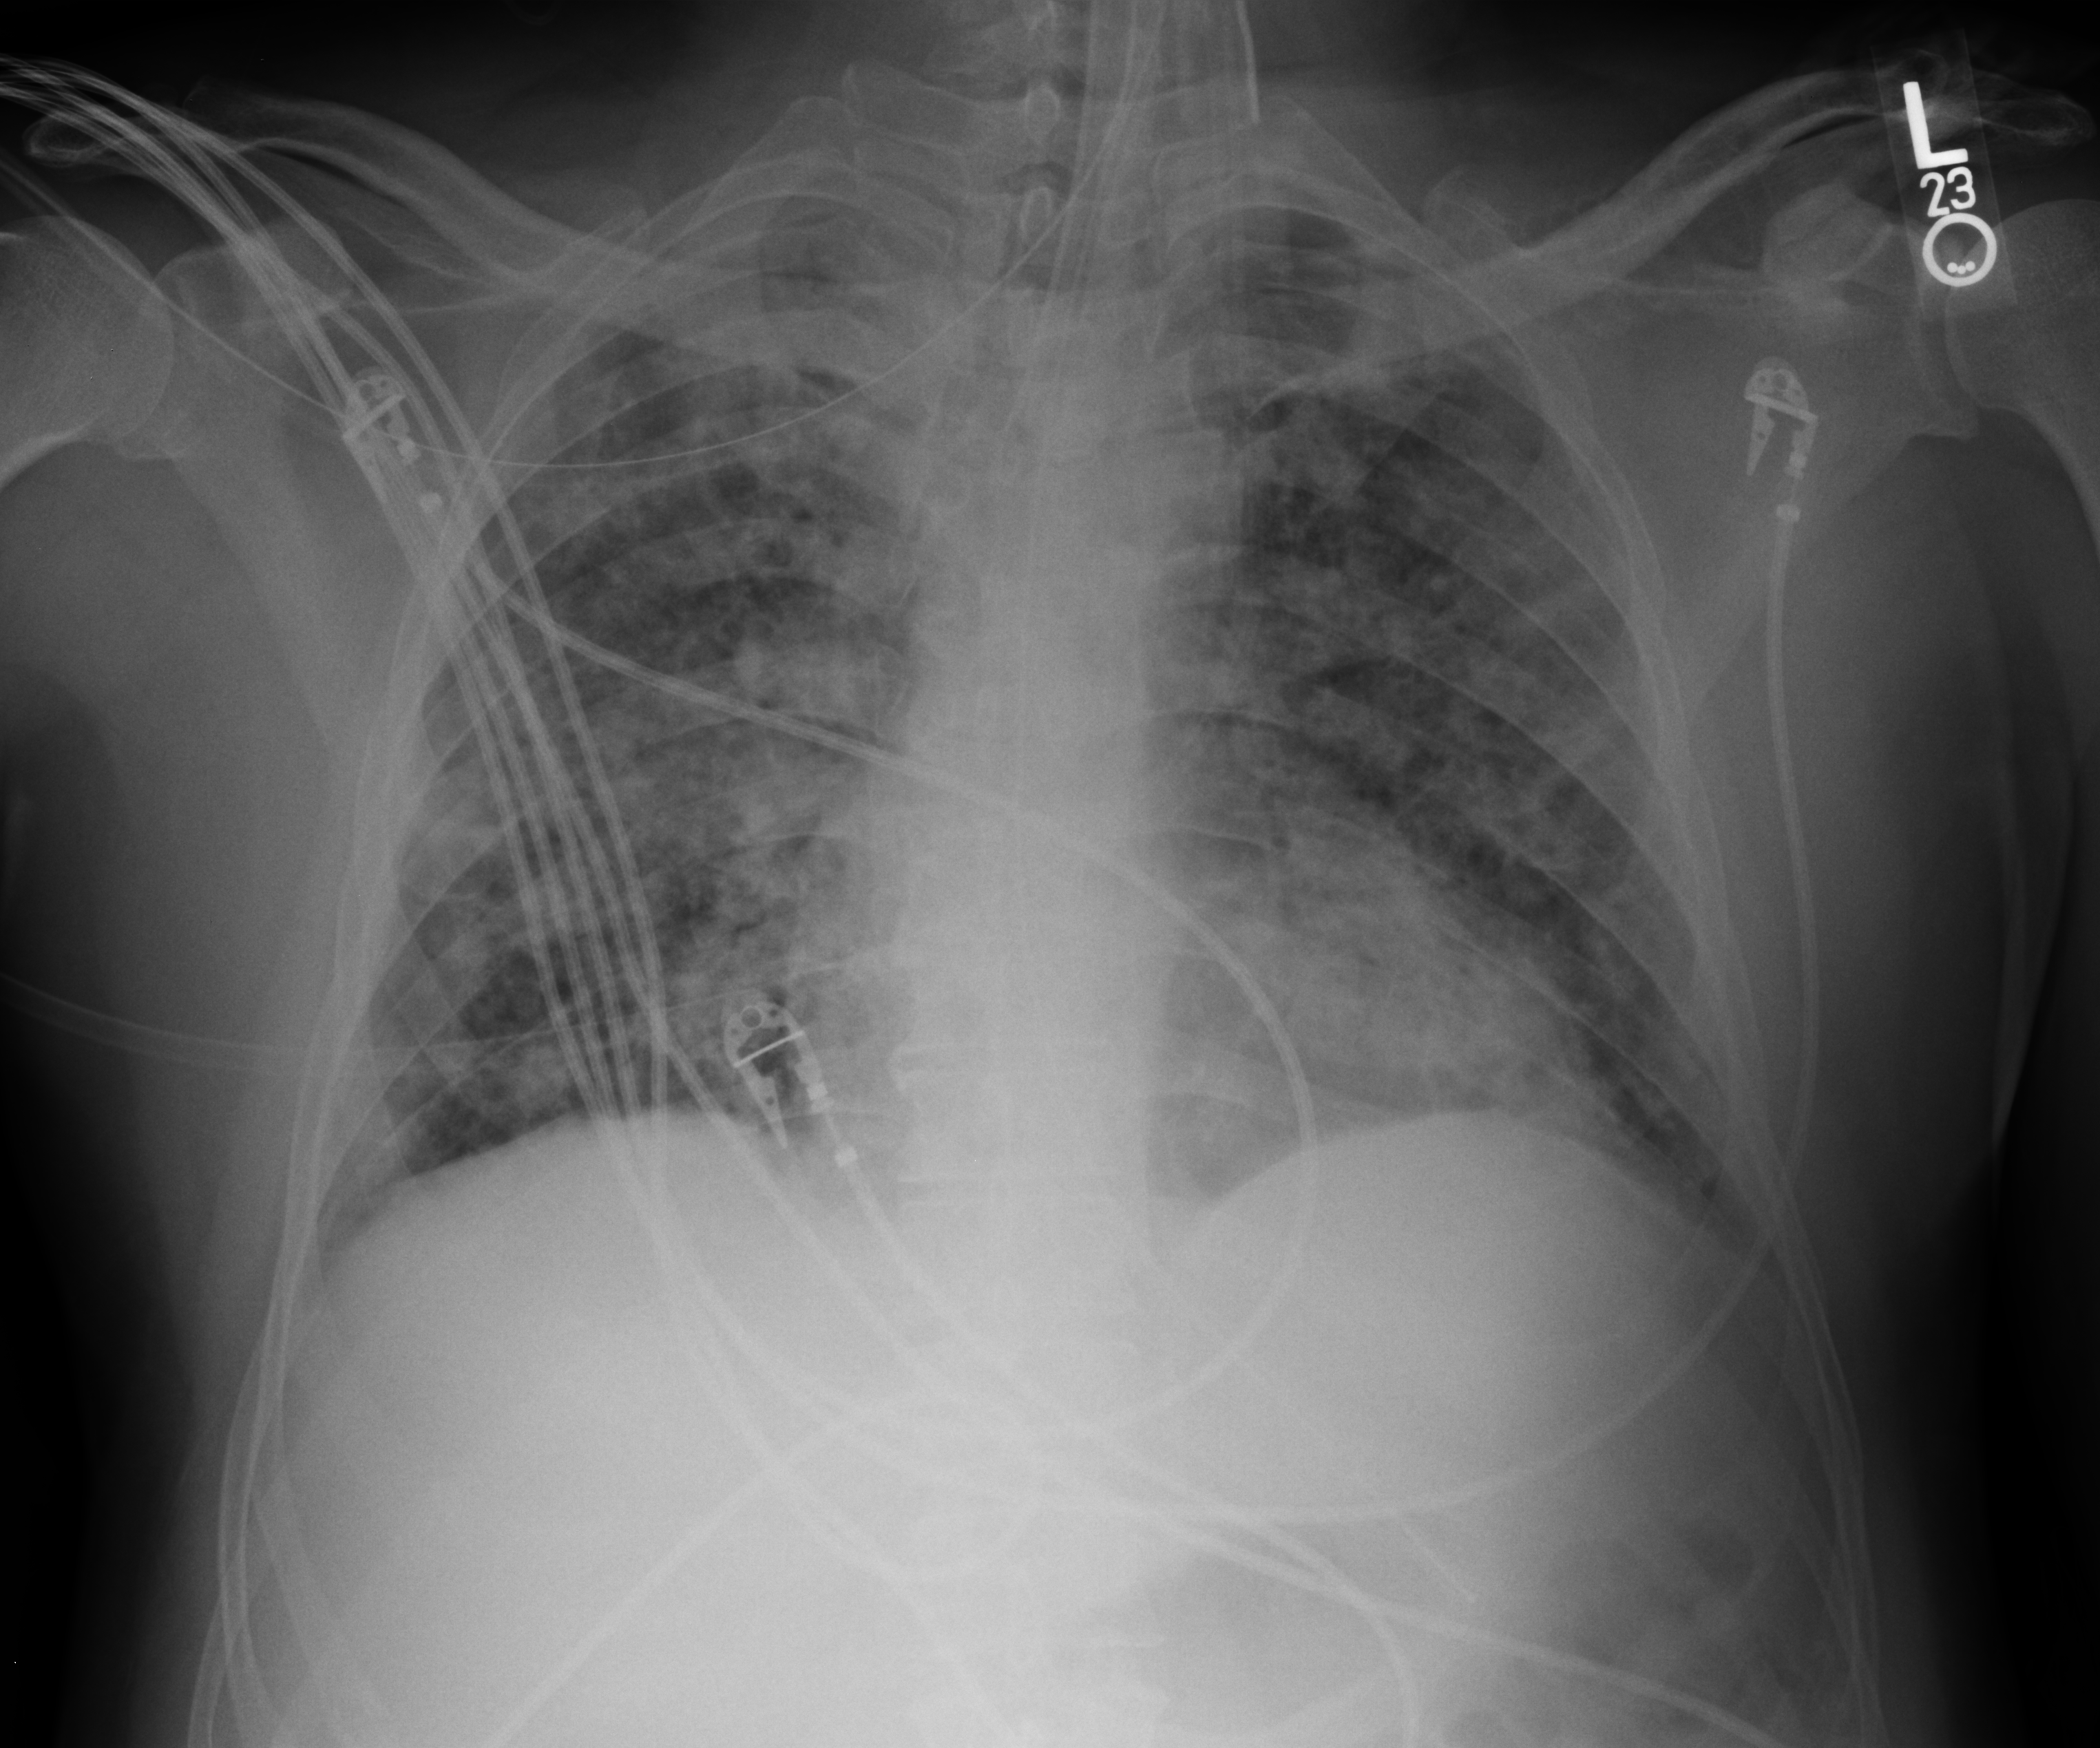
Chest X-ray (portable); anteroposterior (AP) projection. Patient hospitalised with COVID-19; male, aged 18–59 years.
Admission-level facts for this patient (not findings on this image; timing relative to this image not recorded):
- mechanically ventilated during this hospital stay: yes